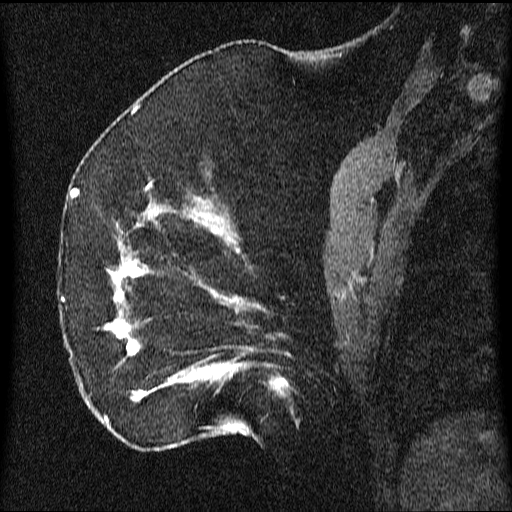
Breast MRI (dynamic contrast-enhanced), one sagittal slice; slice 22 of 64 in the series (ordered by position); dynamic contrast-enhanced series, image 2 of 3 at this slice position (ordered by acquisition); 1.5 T; TE 4.2 ms, TR 9.1 ms; 2.2 mm slice thickness; 512 × 512 image matrix, field of view 180 × 180 mm. Patient: female, 52 years.
Outlined on this slice (semi-automatically segmented with operator editing):
- analysis volume of interest (the breast-tissue region the enhancement analysis was run in; not a lesion): bounding box <61,203,350,438> (left, top, right, bottom; pixels)
- tumour enhancement mask (voxels above the 70 % enhancement threshold inside the analysis volume of interest): <62,207,286,436>